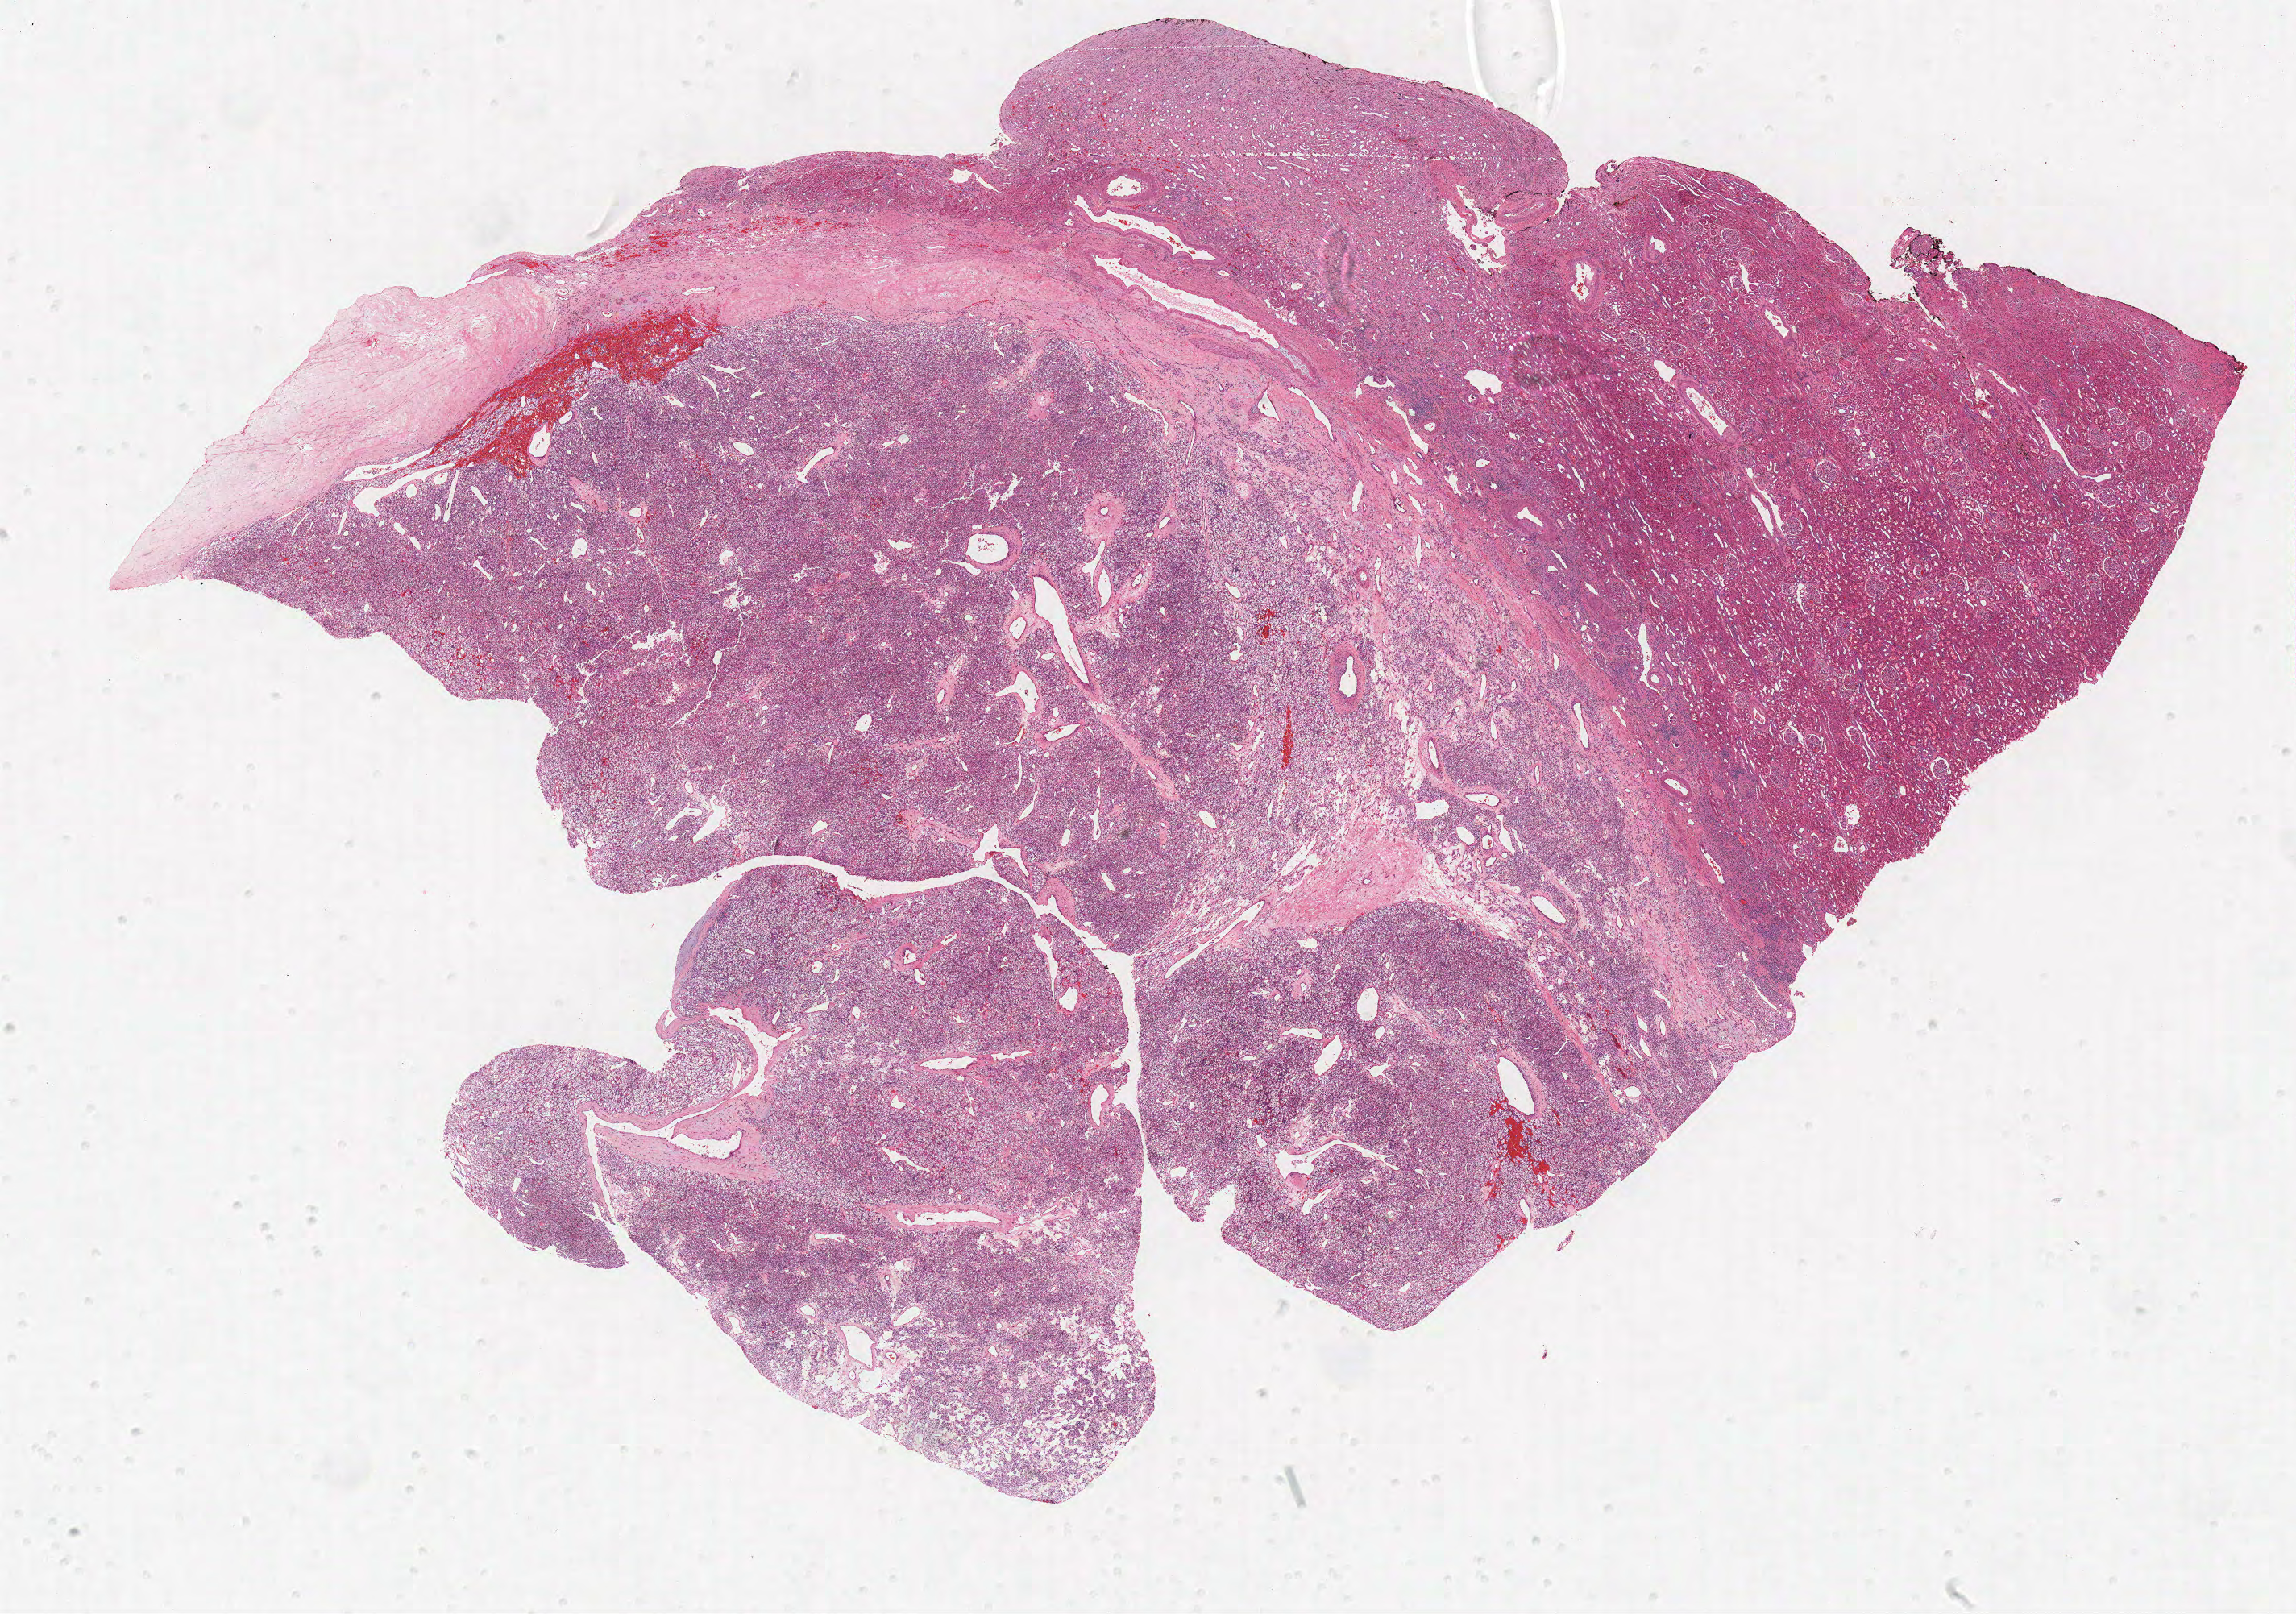
Whole-slide histology image, H&E — low-resolution overview of the scanned area, about 22.8 x 16.0 mm (from a 40x scan); formalin-fixed paraffin-embedded (FFPE) diagnostic section; kidney, primary tumour sample. Male patient; age at initial diagnosis 40 years. Histologic grade: G2 (moderately differentiated).
AJCC pathologic stage: I. Laterality: right. TNM: T1a NX M0. Pathologic diagnosis: Clear cell adenocarcinoma, NOS.